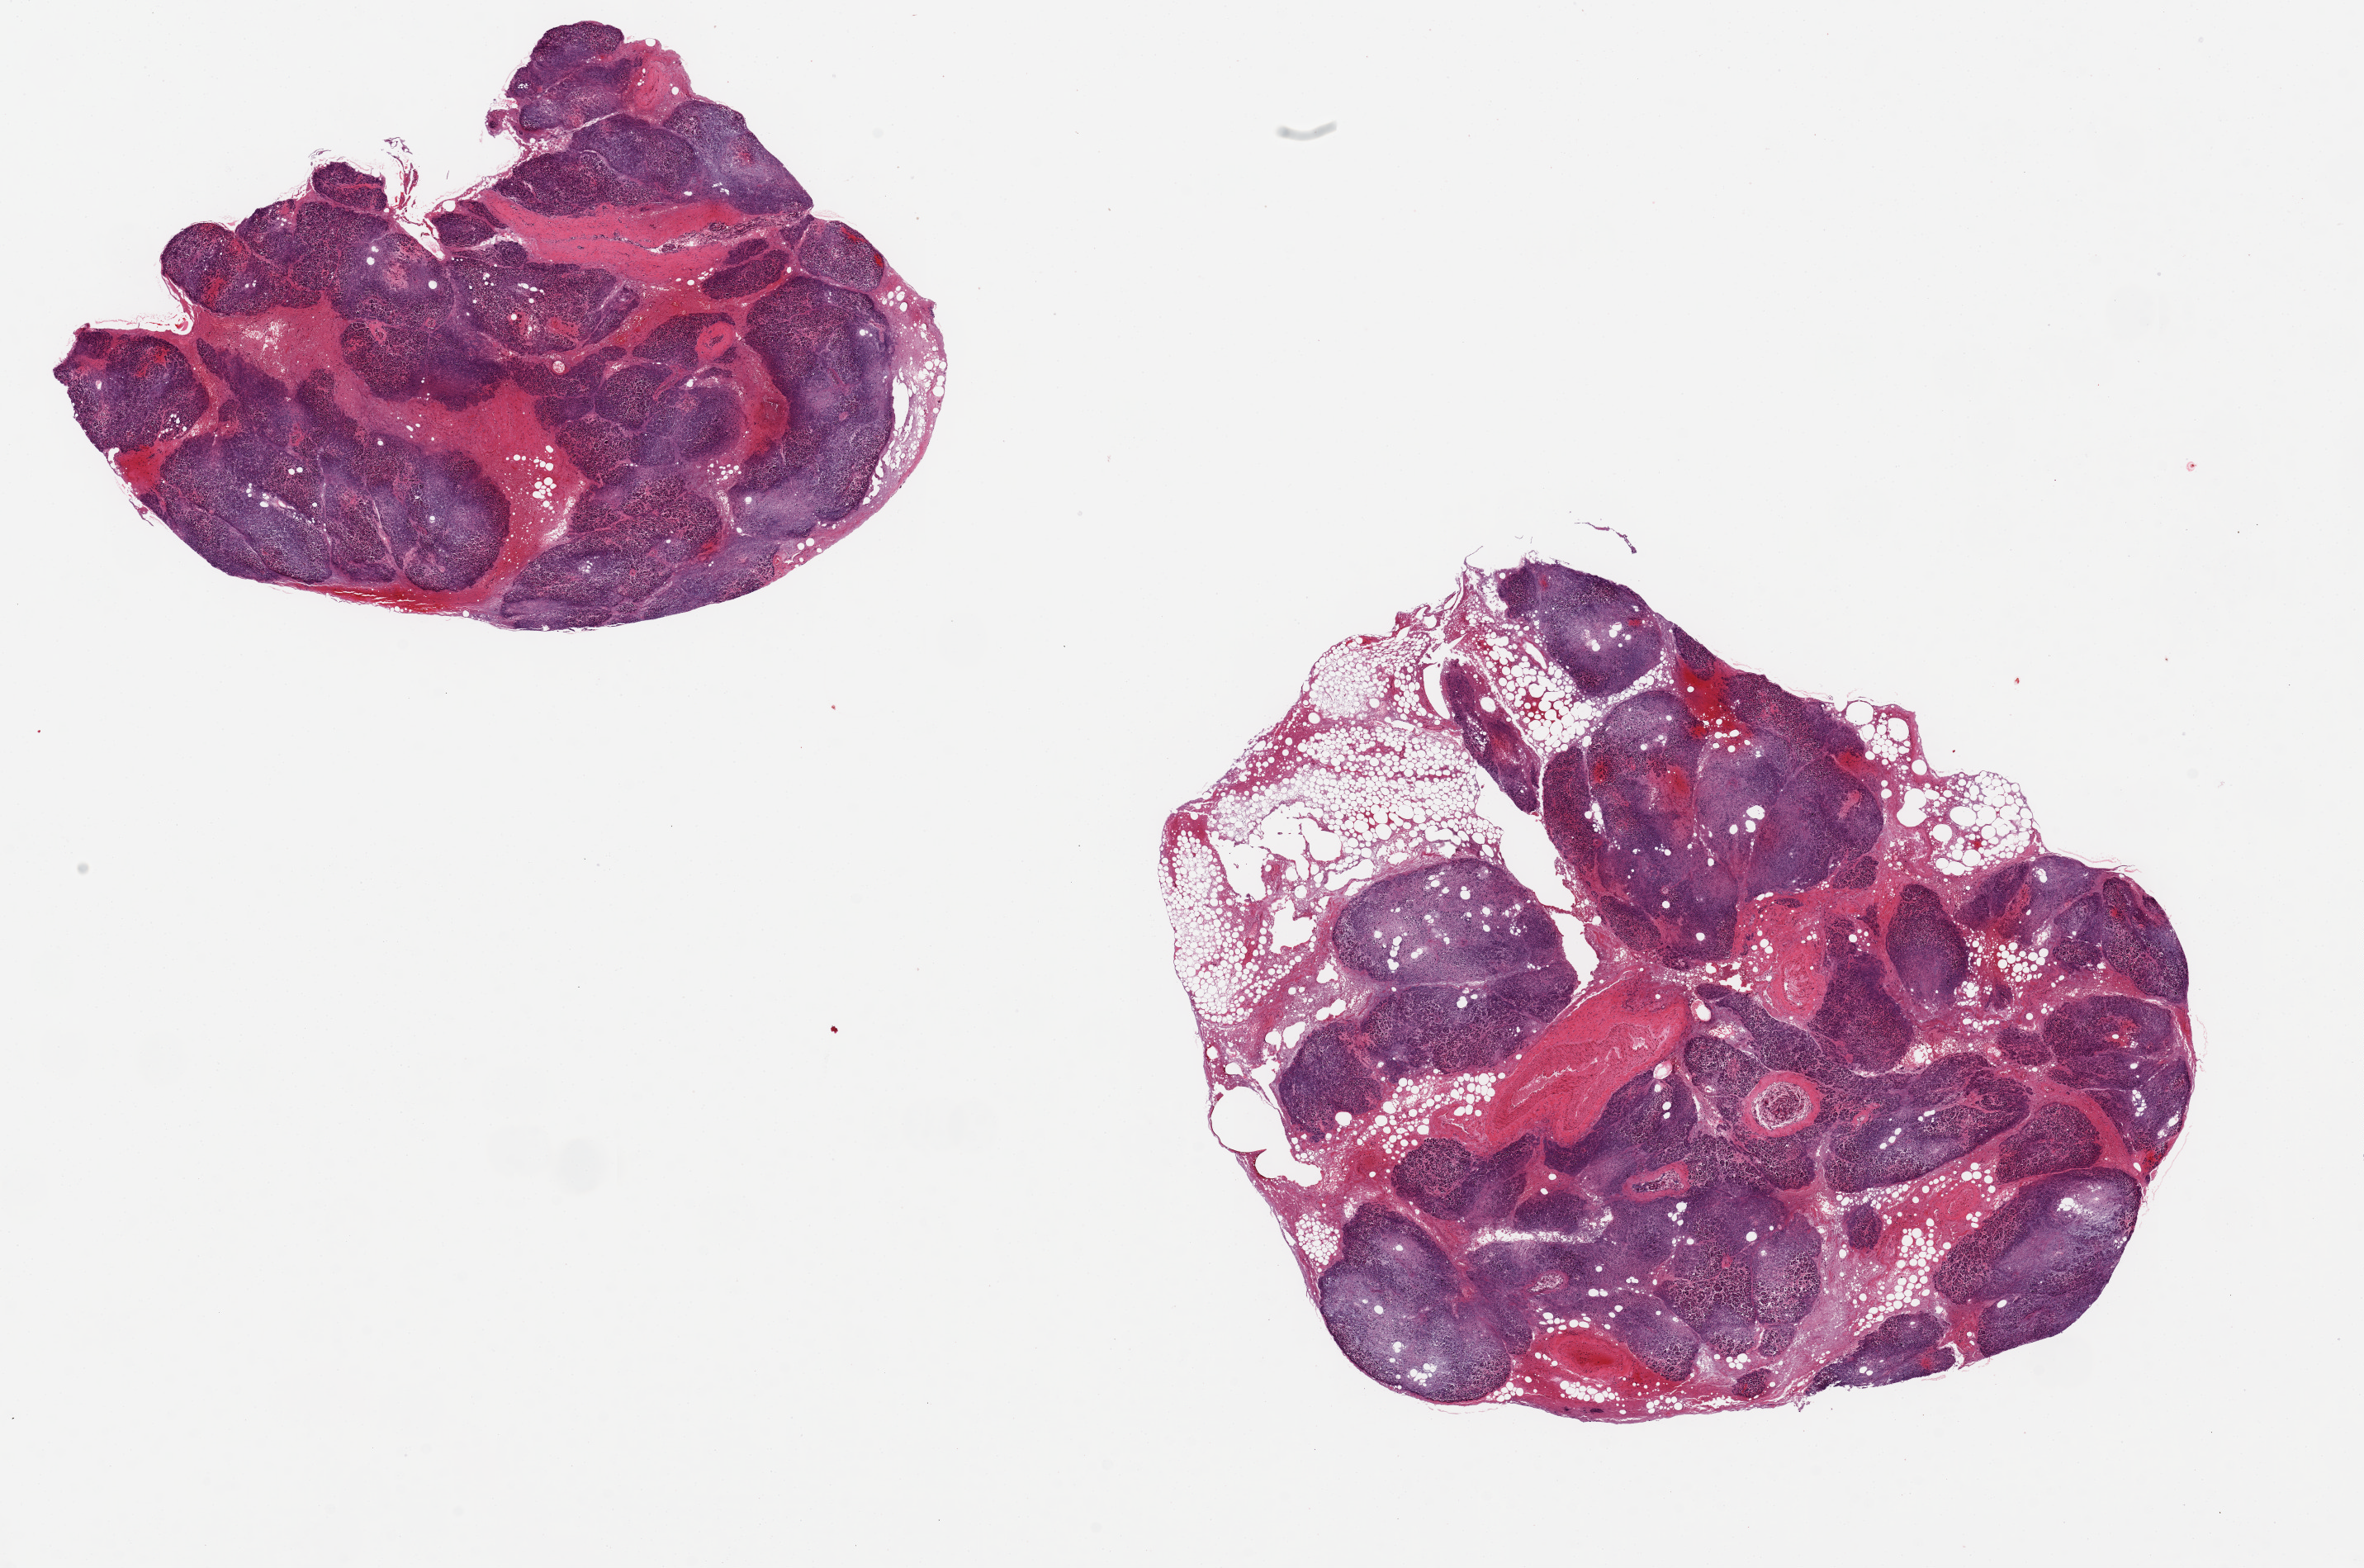
Whole-slide image, haematoxylin and eosin stain, whole scanned area (about 22.6 x 15.0 mm, from a 20x scan) shown as a low-resolution overview. PAXgene-fixed paraffin-embedded (PFPE) section. Target tissue: pancreas. Donor tissue sample.
* review note (as recorded): 2 pieces, 9x8 & 6x5 mm; extensive autolysis